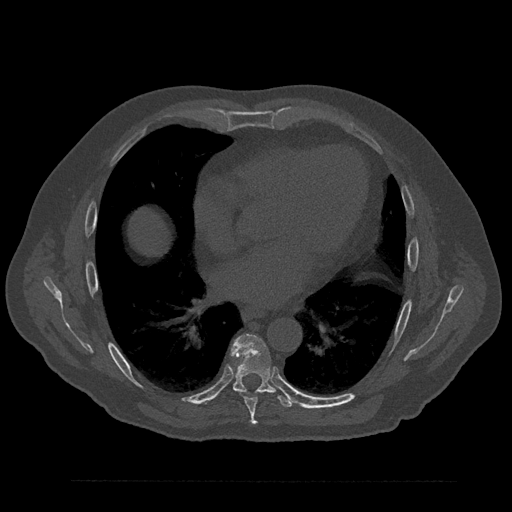
CT including the spine, one axial slice; position 479 of 797 along the scan axis; reconstruction kernel Br40s/3; 120 kVp; bone window (W 1800 / L 400 HU); 0.5 mm slice thickness; 512 × 512 image matrix. Patient: male, 61 years. Case-level facts recorded for this patient, not image findings: primary cancer: prostate.
Structures marked on this image (semi-automatic segmentation, software-assisted and operator-edited):
- T7 vertebra: bounding box (x1, y1, x2, y2) in pixels: (239, 391, 260, 425)
- T8 vertebra: (231, 335, 295, 408)